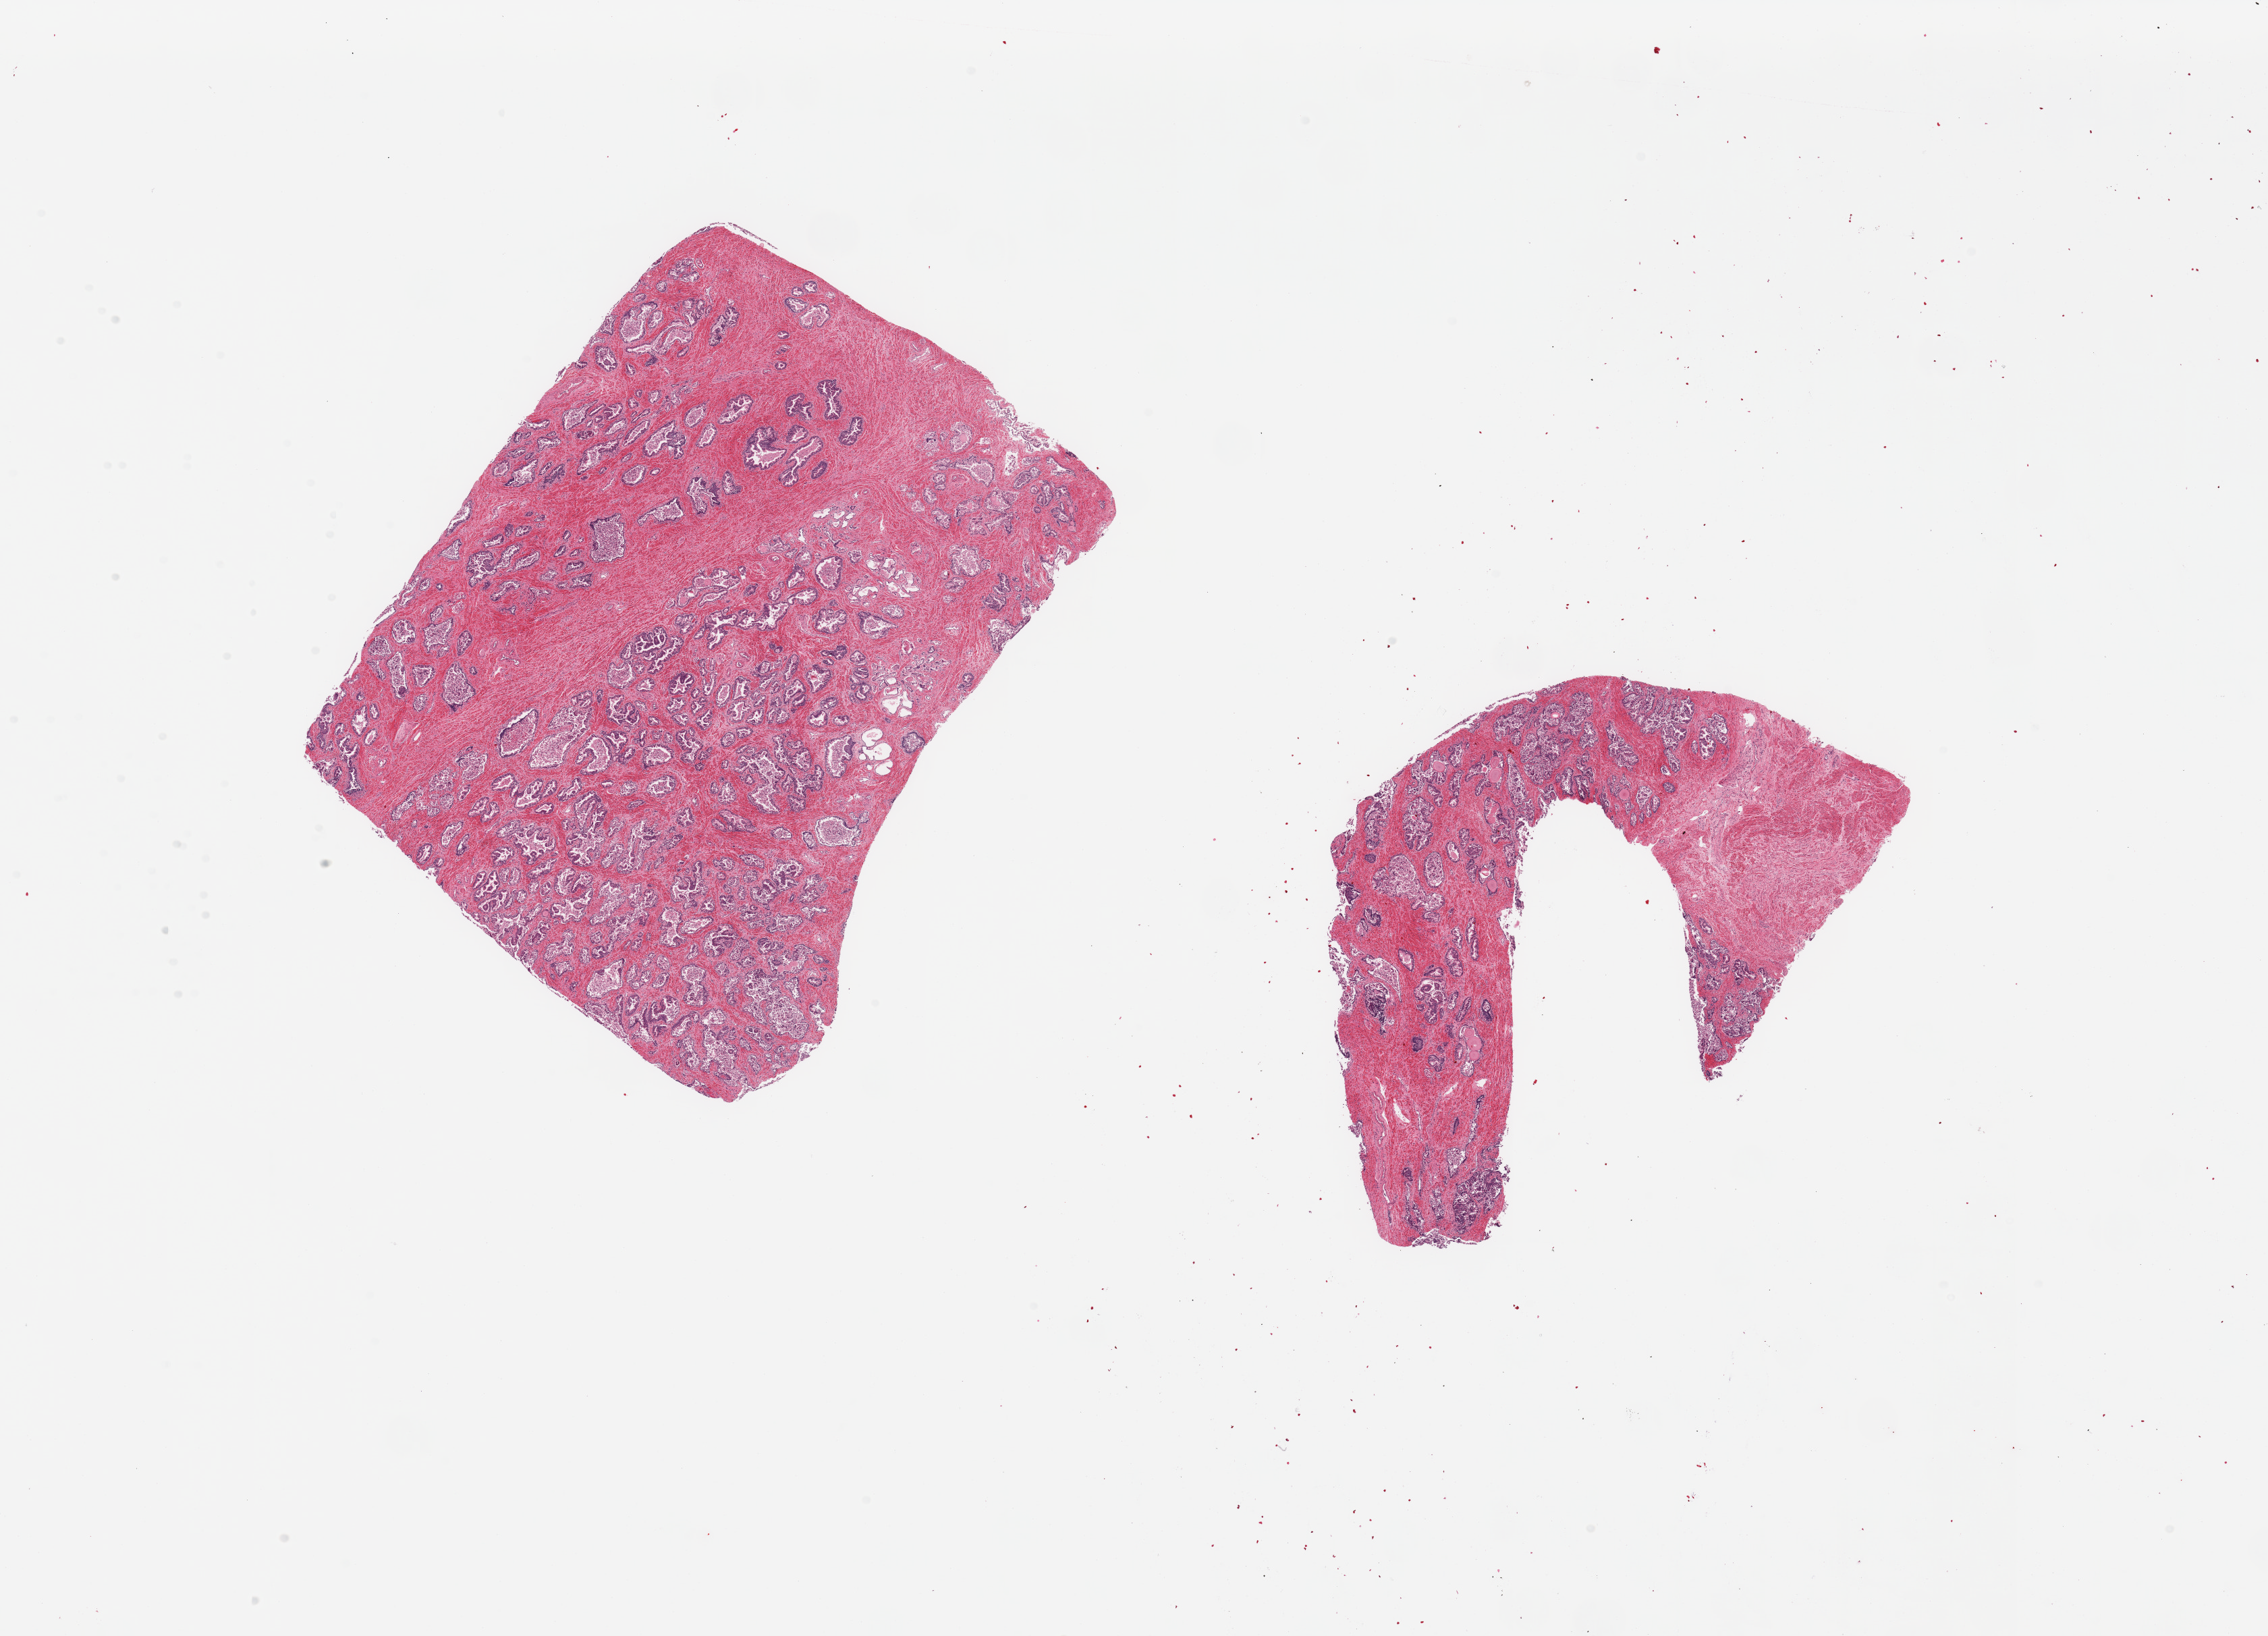
Whole-slide image, H&E stain — a low-resolution overview of the entire scanned area, about 26.6 x 19.2 mm; PAXgene-fixed, paraffin-embedded tissue; target tissue: prostate; tissue donor sample. Donor sex: male.
Reviewer comment on this tissue sample: 2 pieces, glandular elements with moderate autolysis.